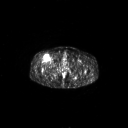
FDG PET of an extremity soft-tissue mass (from a PET/CT study), one axial slice. Slice 305 of 311 in the series (ordered by position). 3.27 mm slice thickness. 128 × 128 image matrix, field of view 700 × 700 mm. Male patient, age 56 years. Case-level facts recorded for this patient, not image findings: histological type: pleiomorphic leiomyosarcoma; grade: intermediate; site of the primary tumour: right thigh.
Outlined on this slice (expert contour drawn on MRI and transferred to this co-registered scan by the dataset authors):
- gross tumour volume including surrounding oedema: bounding box <42,54,50,63> (left, top, right, bottom; pixels)
- gross tumour volume (mass): <44,56,50,62>